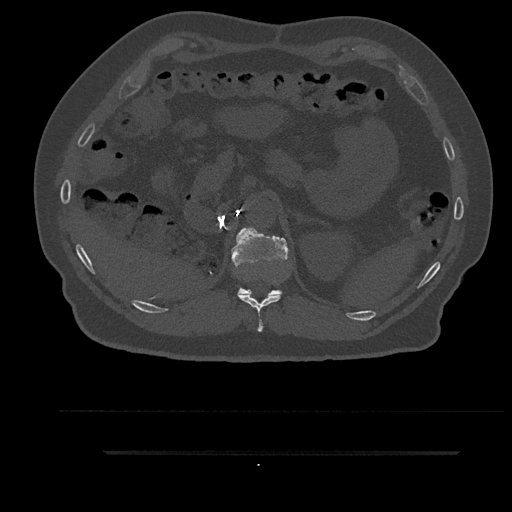
CT including the spine, one axial slice; position 274 of 797 along the scan axis; bone window (W 1800 / L 400 HU); 512 × 512 image matrix, field of view 432 × 432 mm. Patient: male, 63 years. Case-level facts recorded for this patient, not image findings: primary cancer: renal.
Annotated regions visible in this slice (semi-automatically segmented with operator editing):
- T11 vertebra: bounding box [x1, y1, x2, y2] px = [238, 294, 282, 332]
- T12 vertebra: [231, 227, 288, 295]